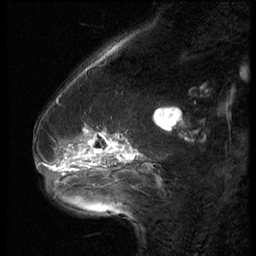
Breast MRI (dynamic contrast-enhanced), one sagittal slice. Slice 19 of 62 in the series (ordered by position). 3 images stored at this slice position (order not interpretable as contrast timing). 1.5 T. TE 4.2 ms, TR 9 ms. 2.5 mm slice thickness. 256 × 256 image matrix. Patient: female, 54 years. From the clinical record (not read from this slice): setting: breast cancer imaged before/during neoadjuvant chemotherapy; receptor status: HR-positive, HER2-negative.
Outlined on this slice (semi-automatically segmented with operator editing):
- analysis volume of interest (the breast-tissue region the enhancement analysis was run in; not a lesion): bounding box [x1, y1, x2, y2] px = [42, 126, 146, 183]
- tumour enhancement mask (voxels above the 140 % enhancement threshold inside the analysis volume of interest): [86, 134, 126, 159]